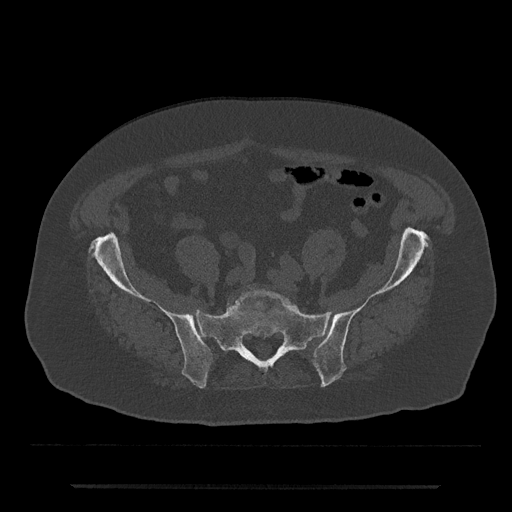
CT including the spine, one axial slice; slice 238 of 797 in the series (ordered by position); reconstruction kernel Br40s/3; bone window (W 1800 / L 400 HU); 512 × 512 image matrix. Patient: male, 80 years. Case-level facts recorded for this patient, not image findings: primary cancer: prostate.
Structures marked on this image (semi-automatic segmentation, software-assisted and operator-edited):
- L5 vertebra: box from (x=232, y=290) to (x=299, y=312) px